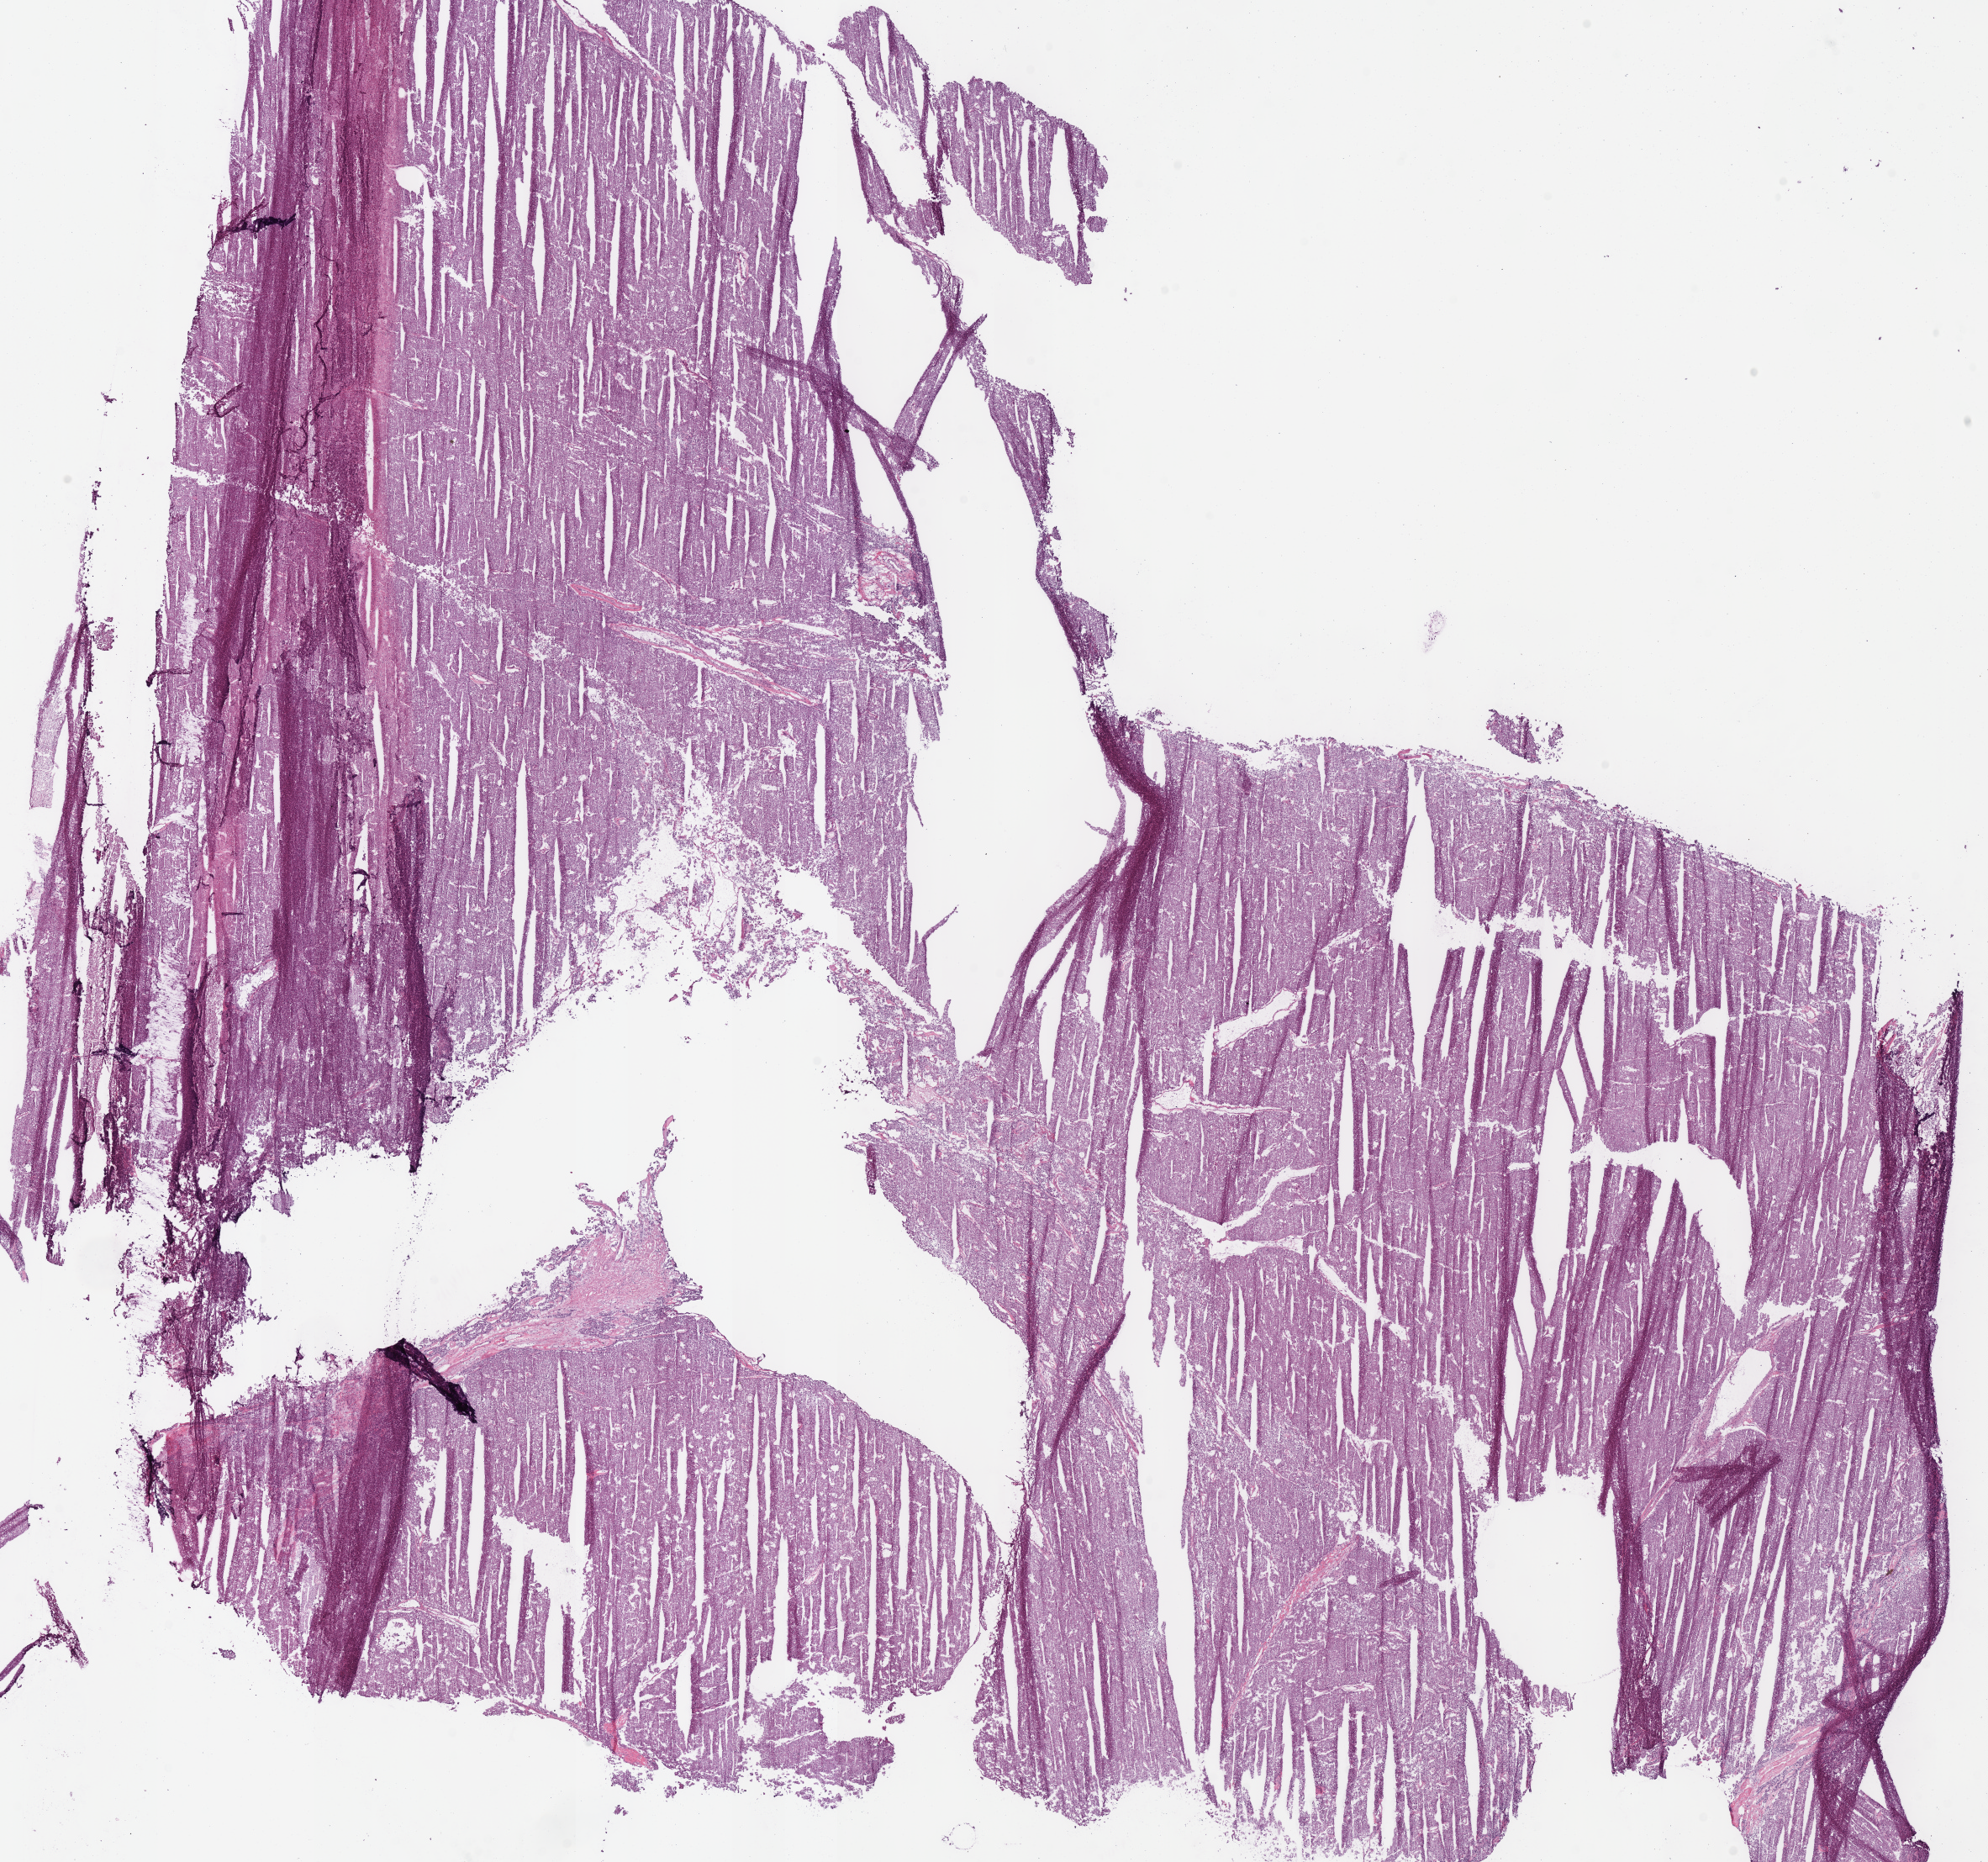
H&E-stained whole-slide image, whole scanned area (about 18.6 x 17.4 mm) shown as a low-resolution overview; frozen section from the bottom of the tissue portion; primary tumour sample from the kidney. Male patient; age at initial diagnosis 60 years. Slide review estimates, as recorded: tumour cells 95%, tumour nuclei 90%, normal cells 0%, stromal cells 5%, necrosis 0%. Inflammatory infiltration, as recorded: lymphocyte infiltration 1%, monocyte infiltration 0%, neutrophil infiltration 0%.
Pathologic diagnosis: Renal cell carcinoma, chromophobe type. TNM: T2b N0 M0. Lymph nodes positive (case pathology): 0 of 4 examined. AJCC pathologic stage: II (6th edition).